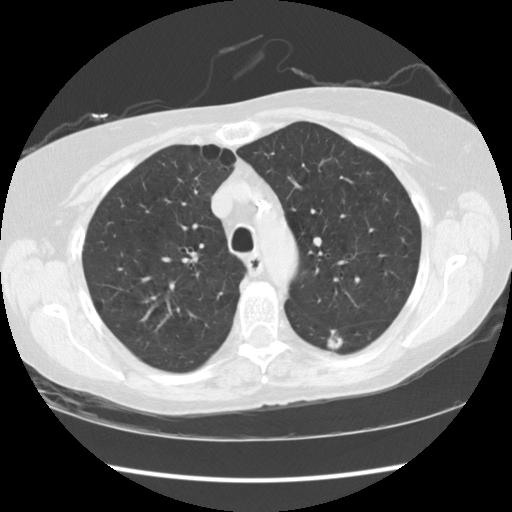
Axial slice from a low-dose chest CT screening exam; third screening round (two years after baseline); lung window (W 1500 / L -600 HU). Female participant, aged 63 years at enrolment. Current smoker at enrolment.
• Lesion marked by an expert reader, box from (x=310, y=321) to (x=358, y=360) px.
• The screening reader recorded 4 non-calcified nodules or masses ≥4 mm on this exam (left lower lobe, right upper lobe, left upper lobe, left lower lobe); which of them this box marks is not recorded.
• Official screen result: positive, other.